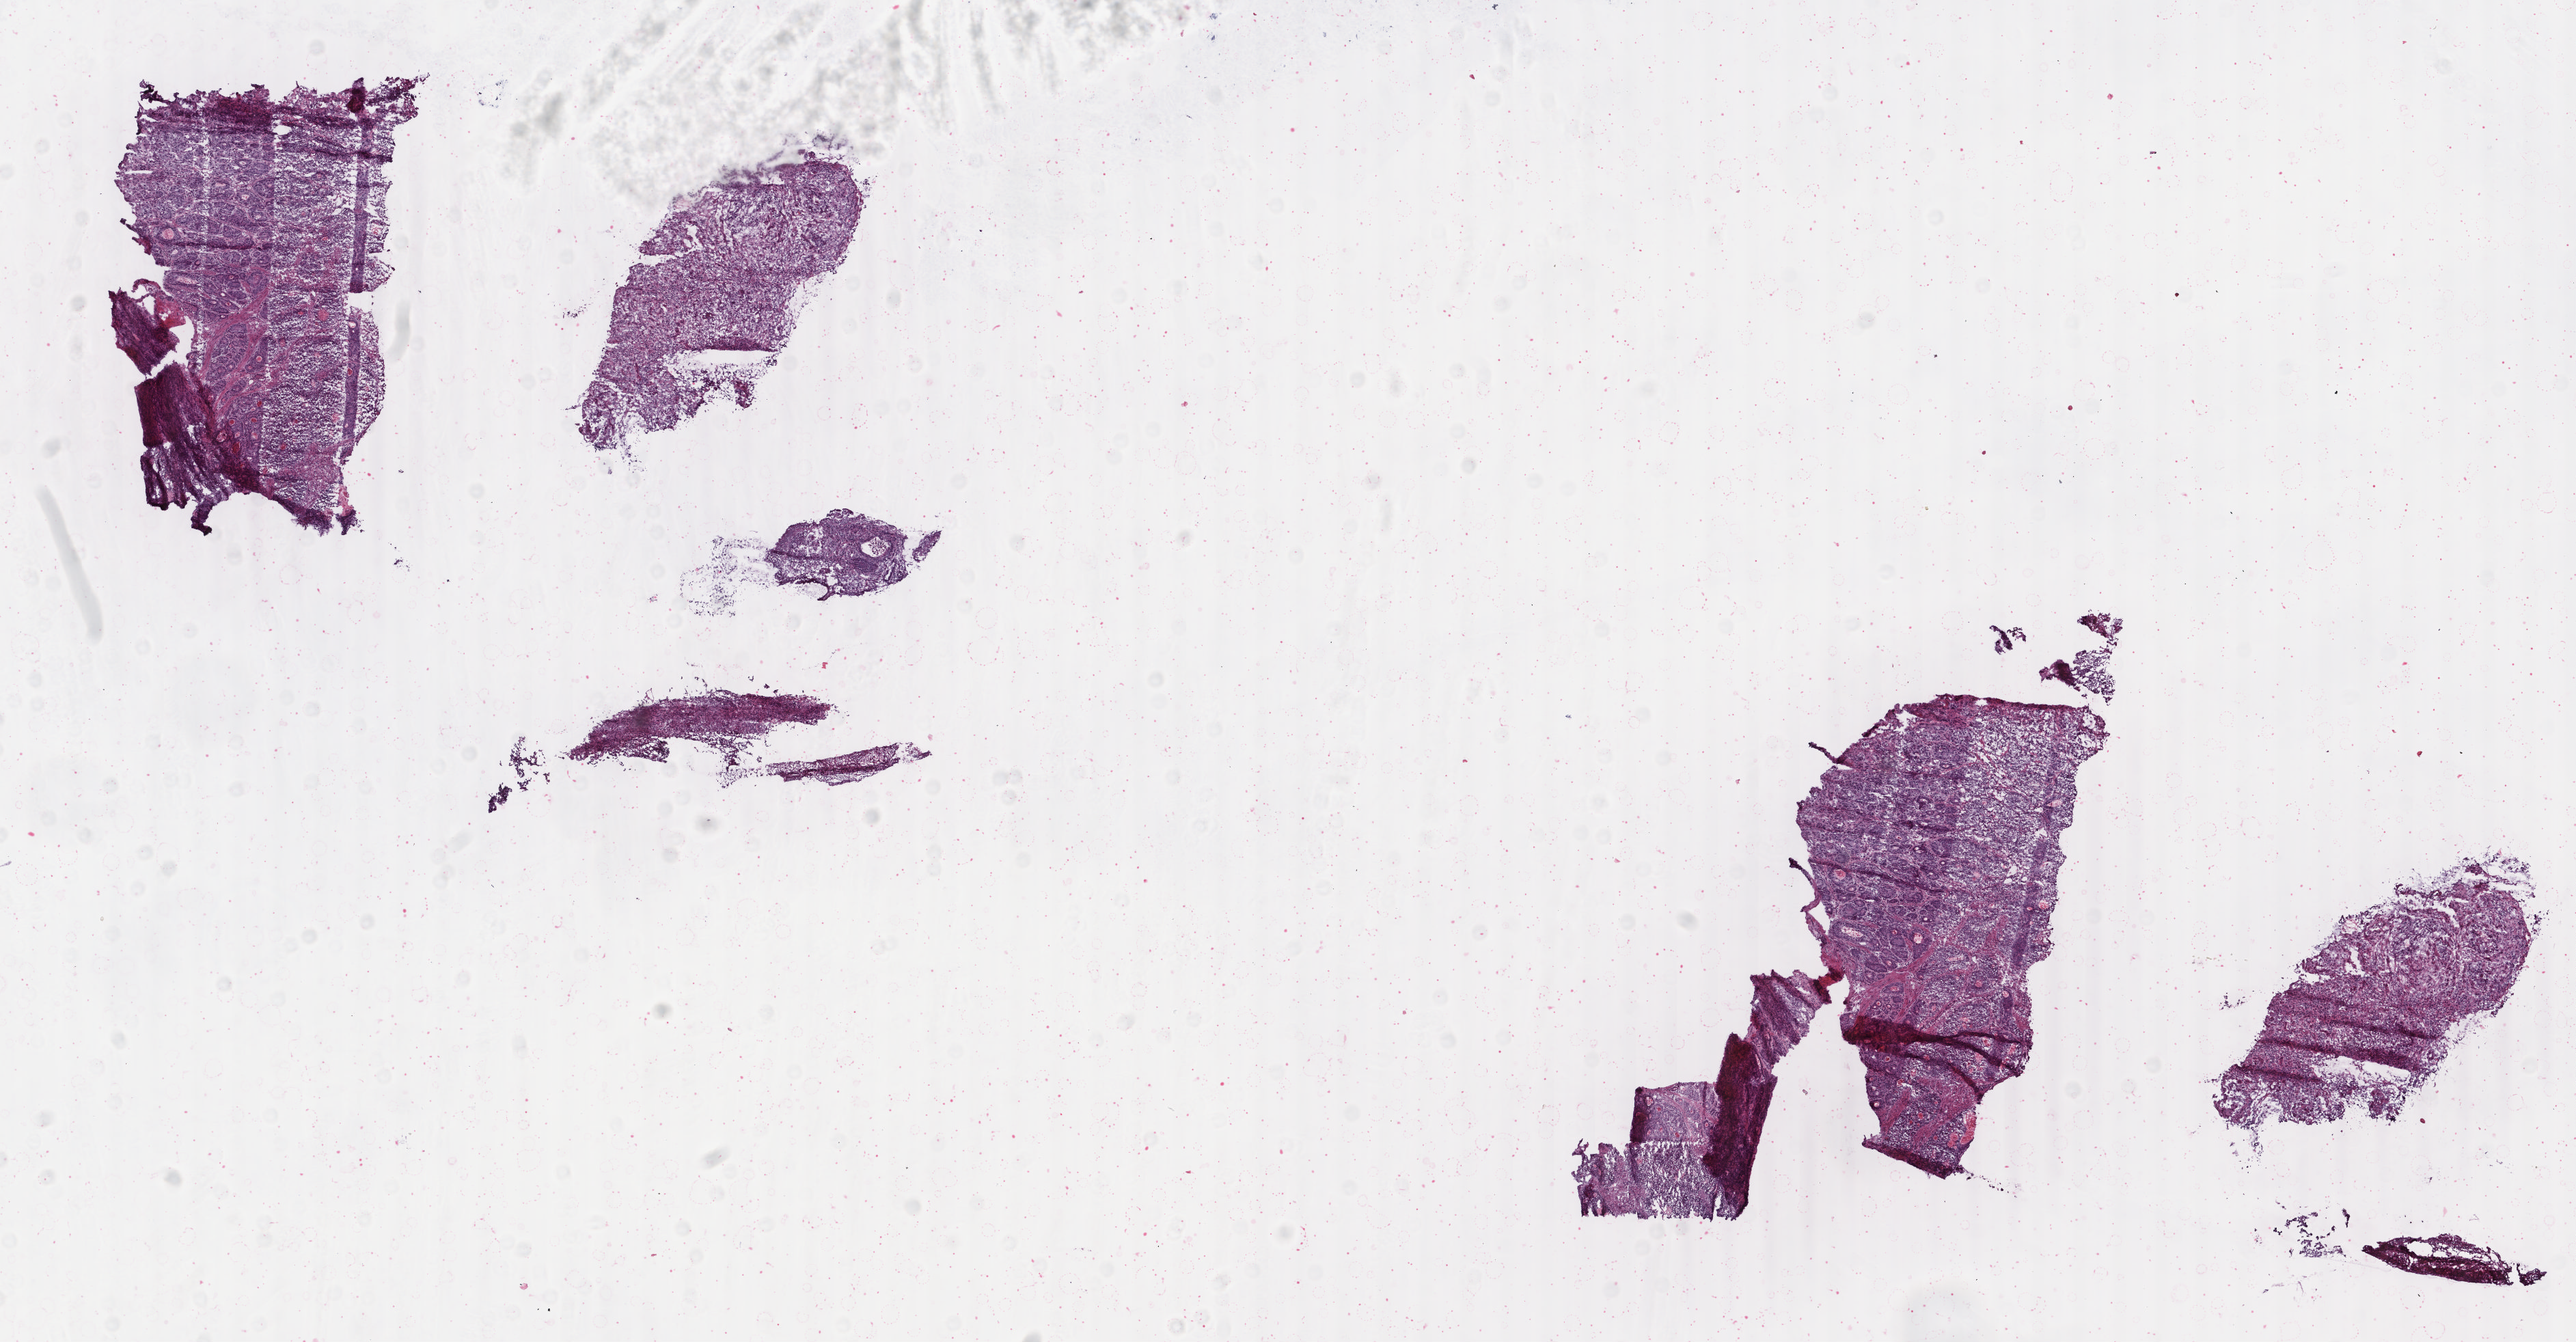
H&E-stained whole-slide image, whole scanned area (about 15.0 x 7.8 mm) shown as a low-resolution overview; frozen section from the bottom of the tissue portion; primary tumour sample from the colon. Female patient; age at initial diagnosis 83 years. Slide review estimates, as recorded: tumour cells 80%, tumour nuclei 90%, normal cells 0%, stromal cells 19%, necrosis 1%. Infiltration values recorded for this section: lymphocyte infiltration 5%, monocyte infiltration 1%, neutrophil infiltration 0%.
AJCC pathologic stage: IIIC (6th edition). Histologic diagnosis: Adenocarcinoma, NOS (sigmoid colon). Lymph nodes positive (case pathology): 32 of 40 examined.